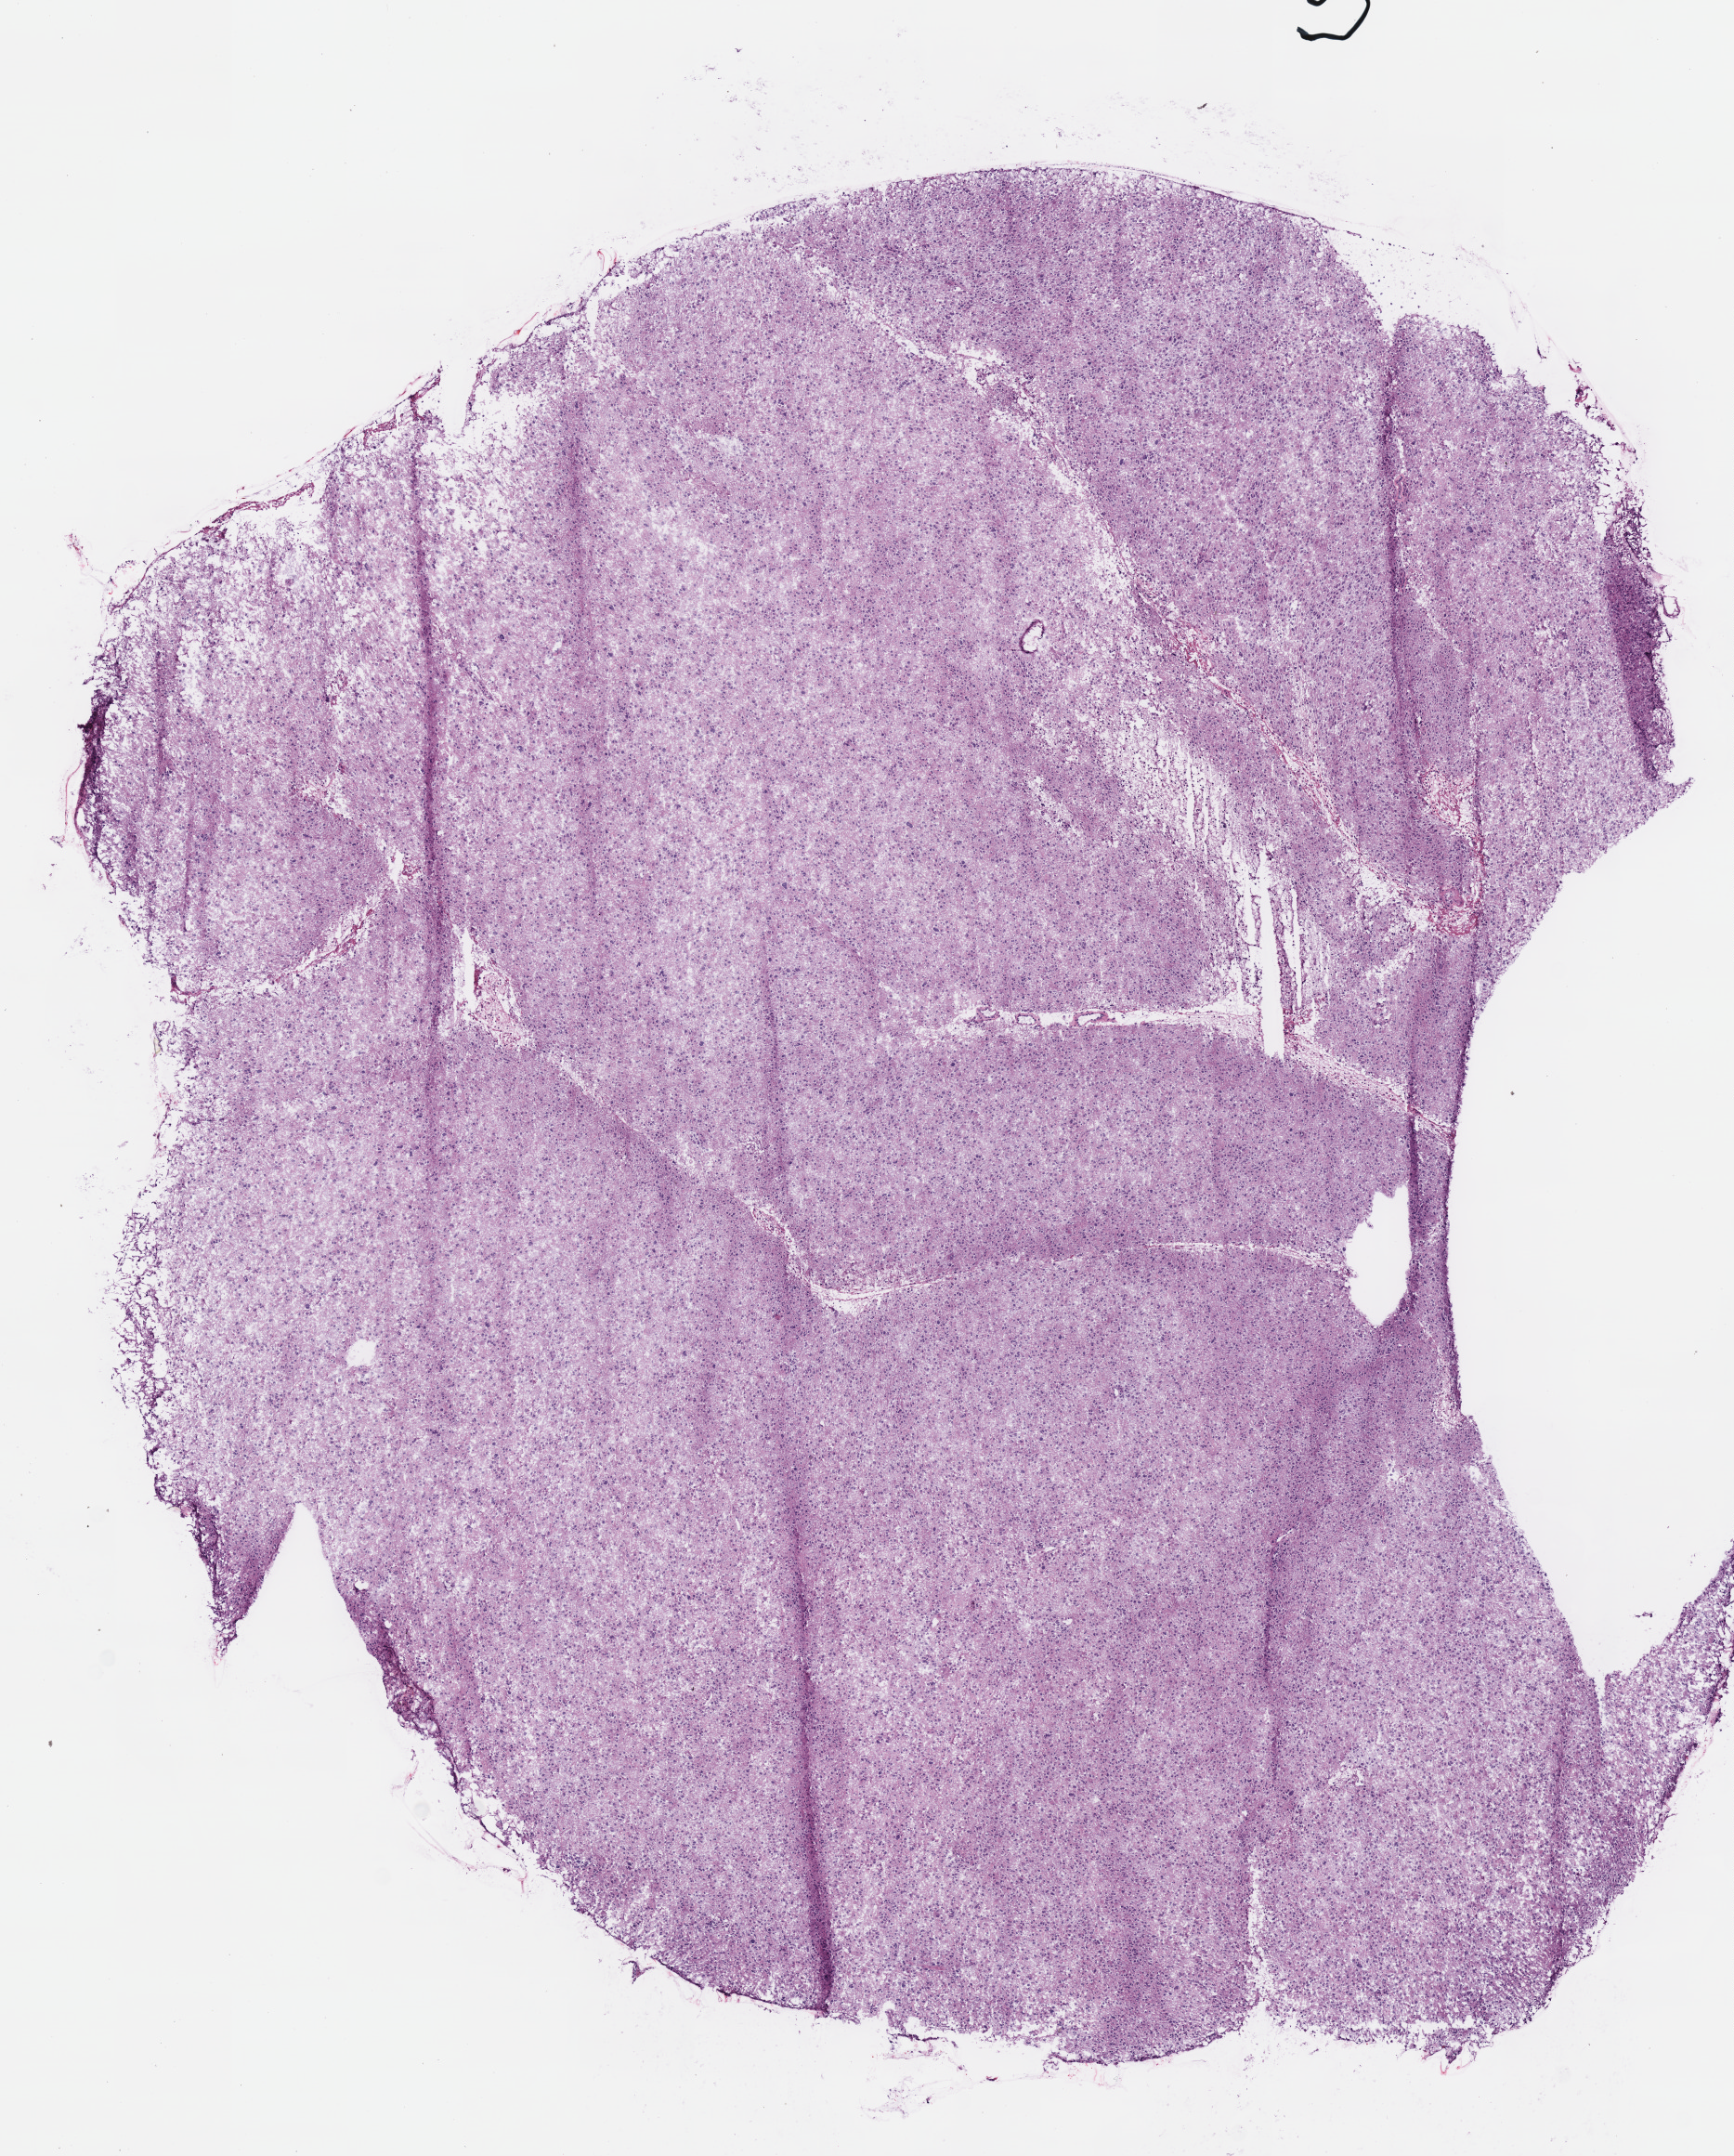
H&E whole-slide image, whole scanned area (about 7.3 x 9.1 mm, from a 40x scan) shown as a low-resolution overview; frozen section from the bottom of the tissue portion; brain, primary tumour sample. Male, age 29 years at initial diagnosis. Histologic grade: G2 (moderately differentiated). Pathologist review of this section (percent, as recorded): tumour cells 100%, tumour nuclei 80%, normal cells 0%, stromal cells 0%, necrosis 0%.
Diagnosis: Mixed glioma (cerebrum).